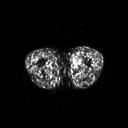
FDG PET of an extremity soft-tissue mass (from a PET/CT study), one axial slice. Position 231 of 311 along the scan axis. 3.27 mm slice thickness. 128 × 128 image matrix, field of view 500 × 500 mm. Patient: male, 29 years. Case-level facts recorded for this patient, not image findings: histological type: mixoid liposarcoma; grade: low; site of the primary tumour: left thigh.
Annotated regions visible in this slice (expert contour drawn on MRI and transferred to this co-registered scan by the dataset authors):
- gross tumour volume (mass): bounding box [x1, y1, x2, y2] px = [72, 56, 81, 67]